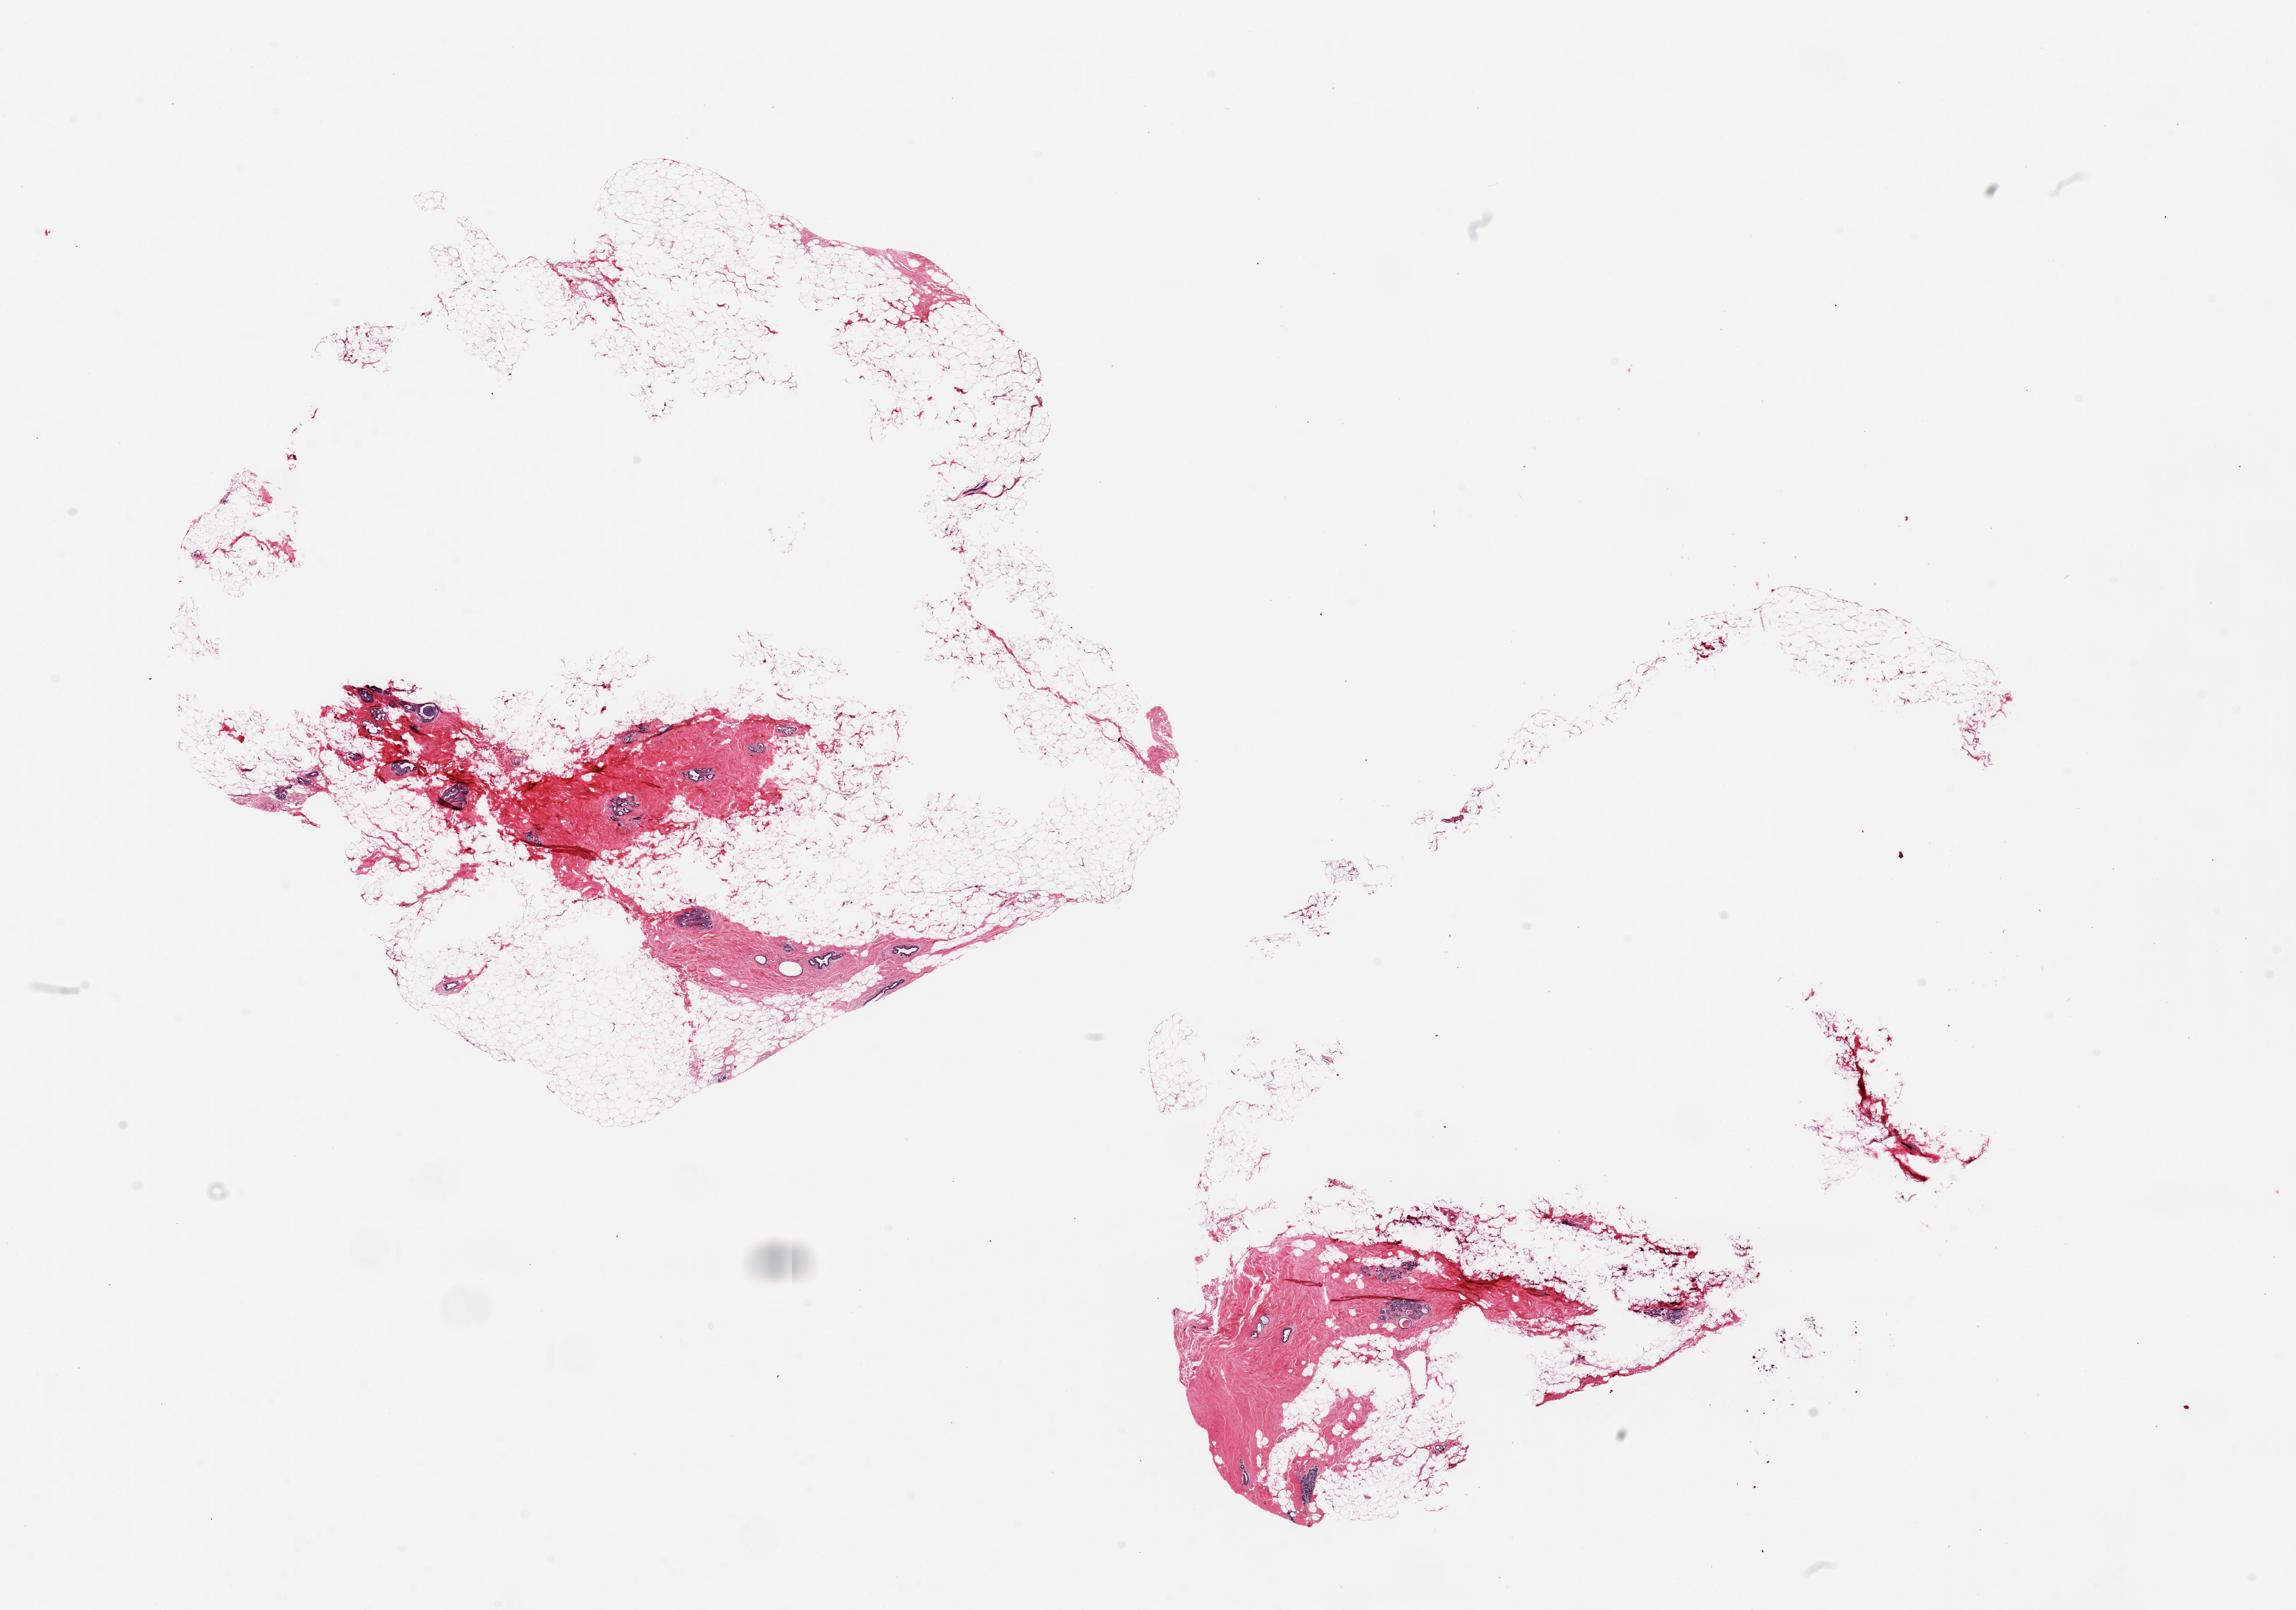
Digitized hematoxylin and eosin (H&E)-stained section, brightfield — low-resolution overview of the scanned area, about 28.5 x 20.0 mm; PAXgene-fixed paraffin-embedded (PFPE) section; target tissue: breast; donor tissue sample. Female donor.
Pathologist's review note for this sample: 2 pieces ~12x8; Extreme separation; A few TDLUs noted; majority of both aliquots is fat (~85%).